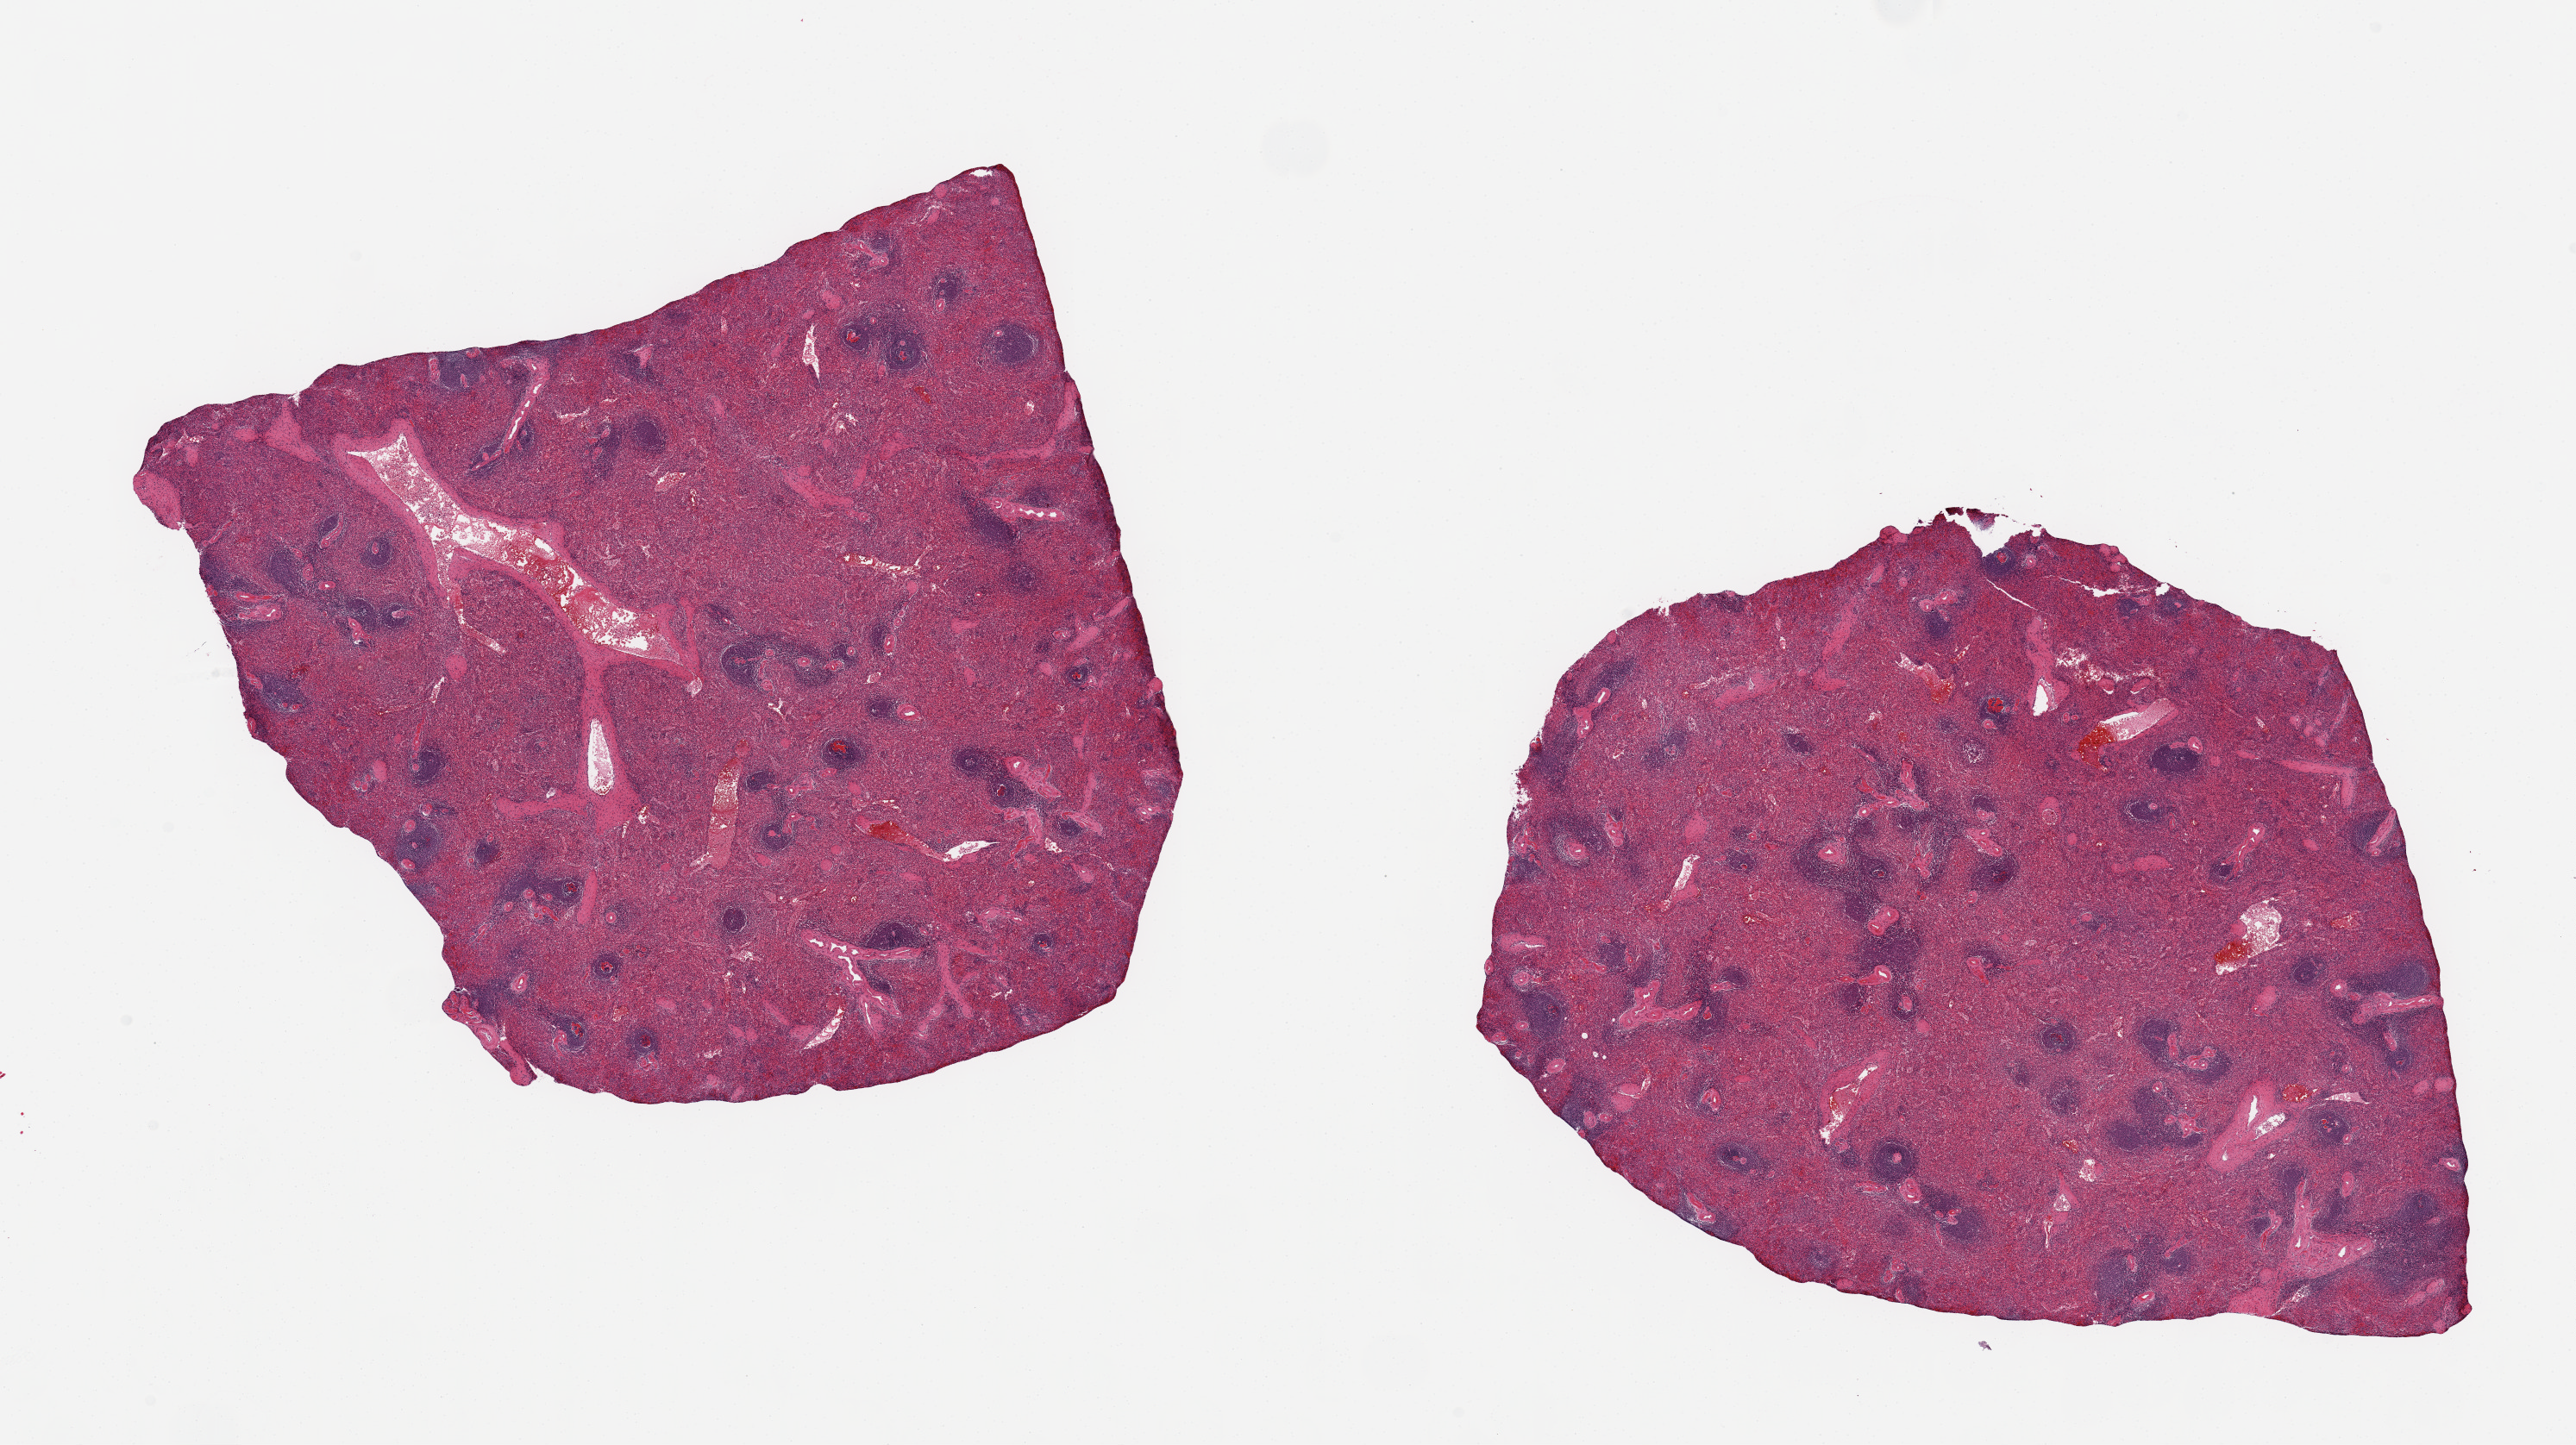
Digitized H&E-stained section, brightfield — a low-resolution overview of the entire scanned area, about 23.6 x 13.3 mm, PAXgene-fixed, paraffin-embedded tissue, target tissue: spleen, tissue donor sample. Donor sex: female.
• pathologist's review note for this sample: 2 pieces, 8x7 & 8x6 mm, no congestion